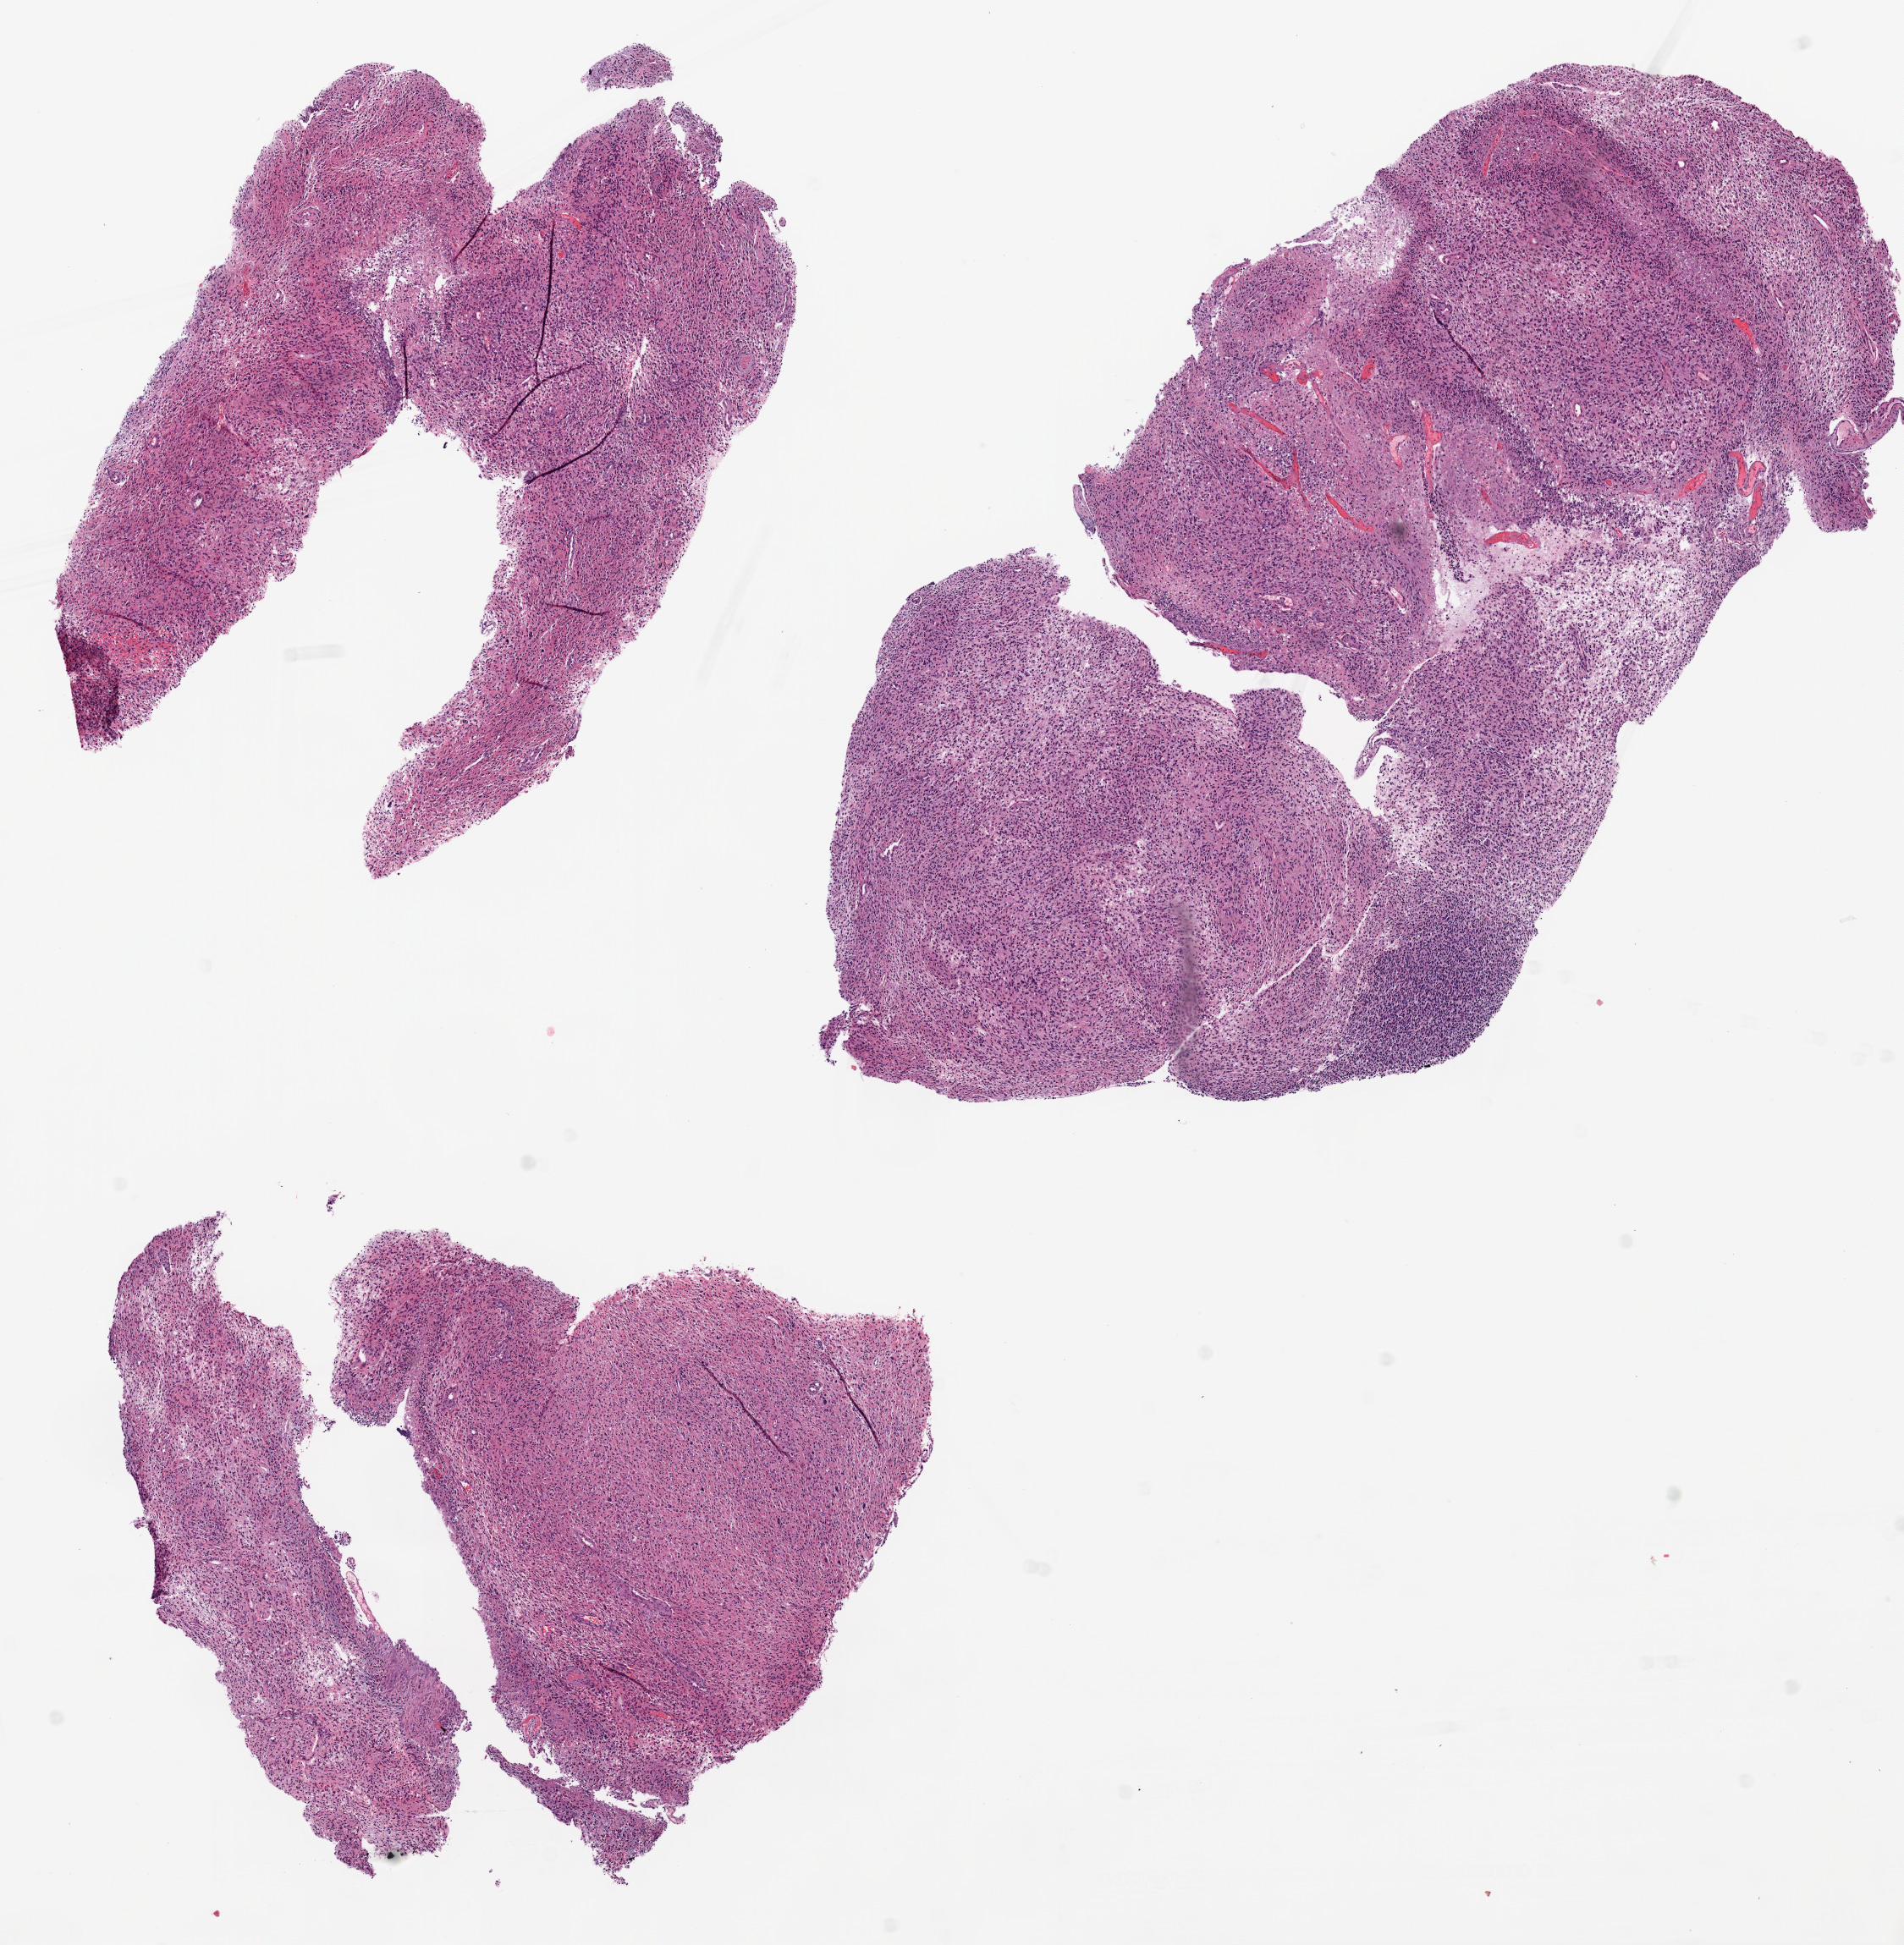
Whole-slide histology image, H&E-stained — a low-resolution overview of the entire scanned area, about 9.0 x 9.2 mm (slide scanned at 20x). Formalin-fixed paraffin-embedded (FFPE) diagnostic section. Primary tumour sample from the brain. Female, age 58 years at initial diagnosis.
Histologic diagnosis: Glioblastoma.